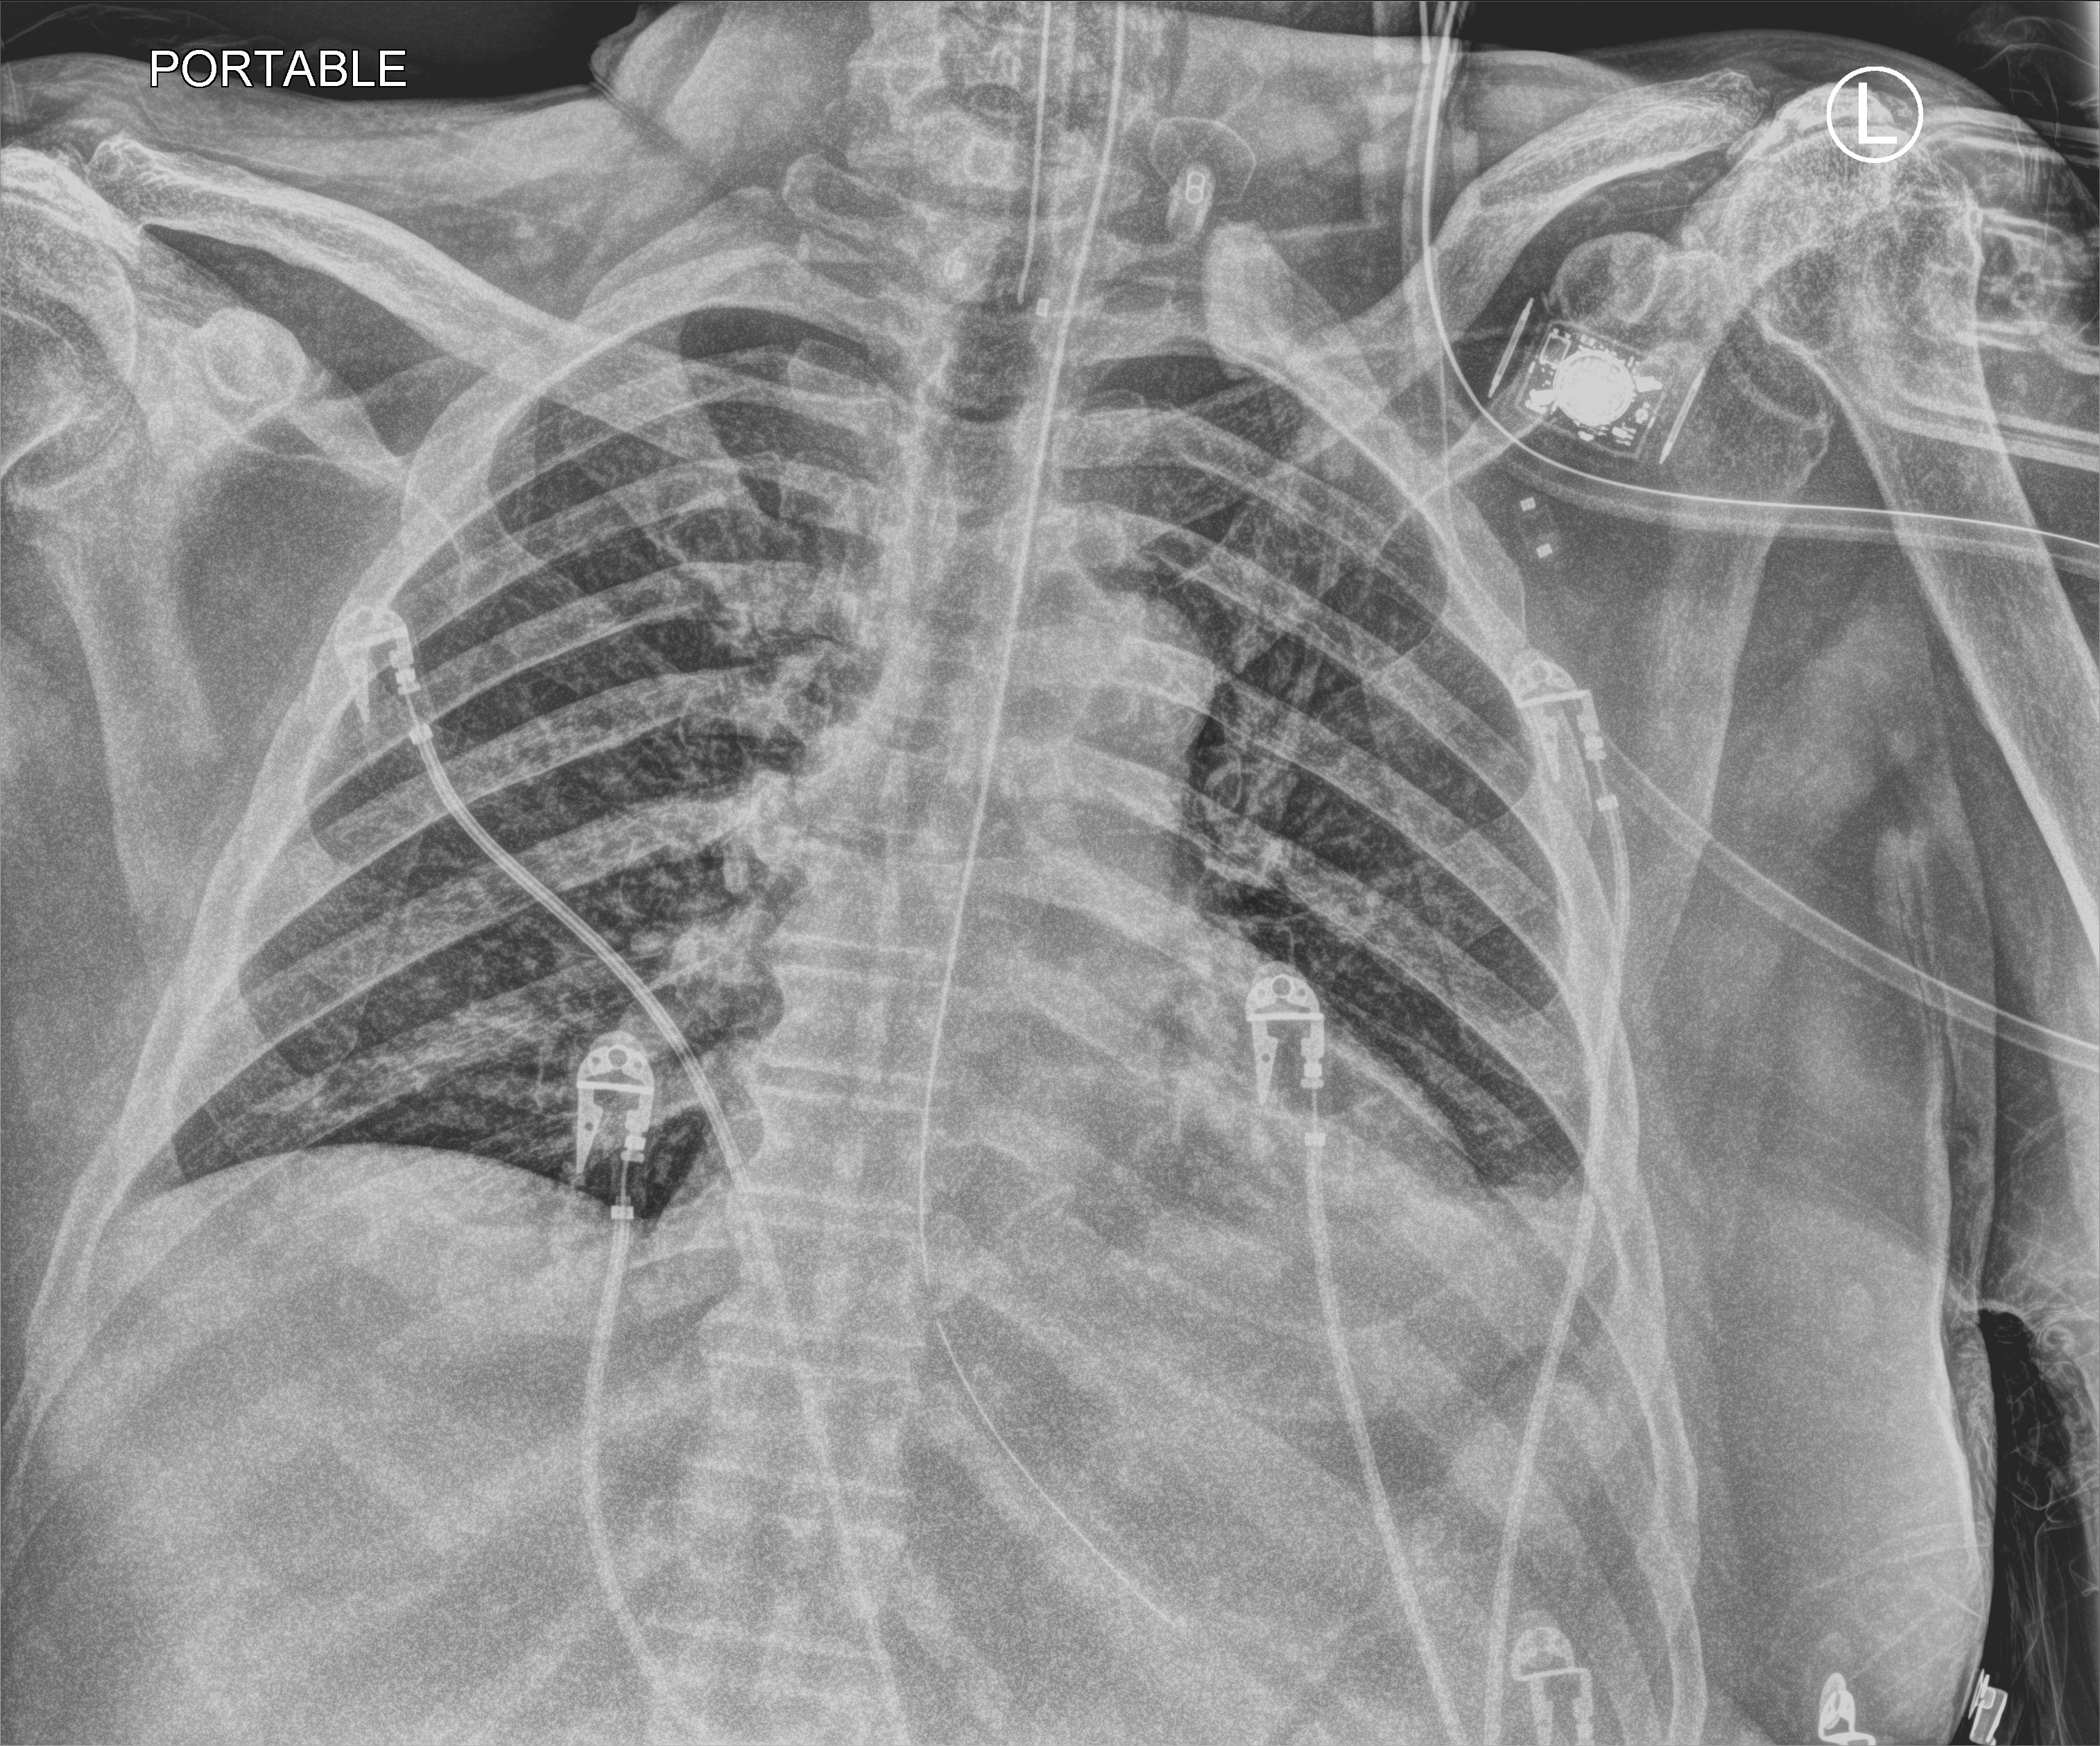
Chest X-ray (portable), anteroposterior (AP) projection. Patient hospitalised with COVID-19; male, aged 75–90 years.
From the hospital-stay record, not from the radiograph (when in the stay this image was taken is not recorded): admitted to intensive care during this hospital stay: yes; mechanically ventilated during this hospital stay: yes; hypertension (admission record): yes.